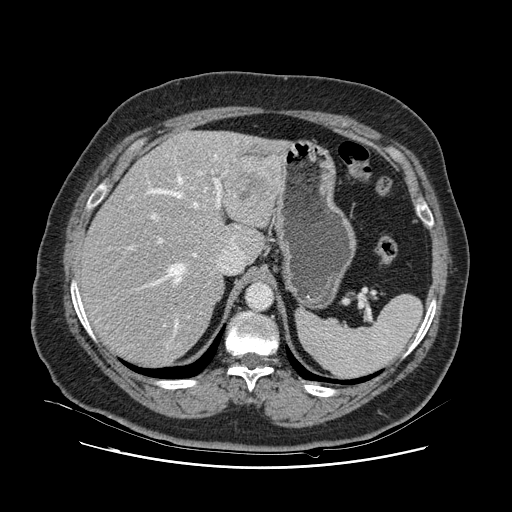
Contrast-enhanced abdominal CT, one axial slice. 120 kVp. Intravenous contrast given. Soft-tissue window (W 400 / L 40 HU). 512 × 512 image matrix, field of view 391 × 391 mm. Female patient, age 73 years. From the clinical record (not read from this slice): diagnosis: colorectal cancer liver metastases, imaged before liver resection; multiple liver metastases: no; largest metastasis: 7 cm; disease in both lobes: no.
Annotated regions visible in this slice (expert manual segmentation):
- hepatic veins: bounding box <129,155,235,334> (left, top, right, bottom; pixels)
- liver: <83,132,283,364>
- planned liver remnant (the part of the liver to remain after resection): <83,160,239,365>
- portal vein (with intrahepatic branches): <127,171,226,327>
- liver metastasis: <238,172,271,203>